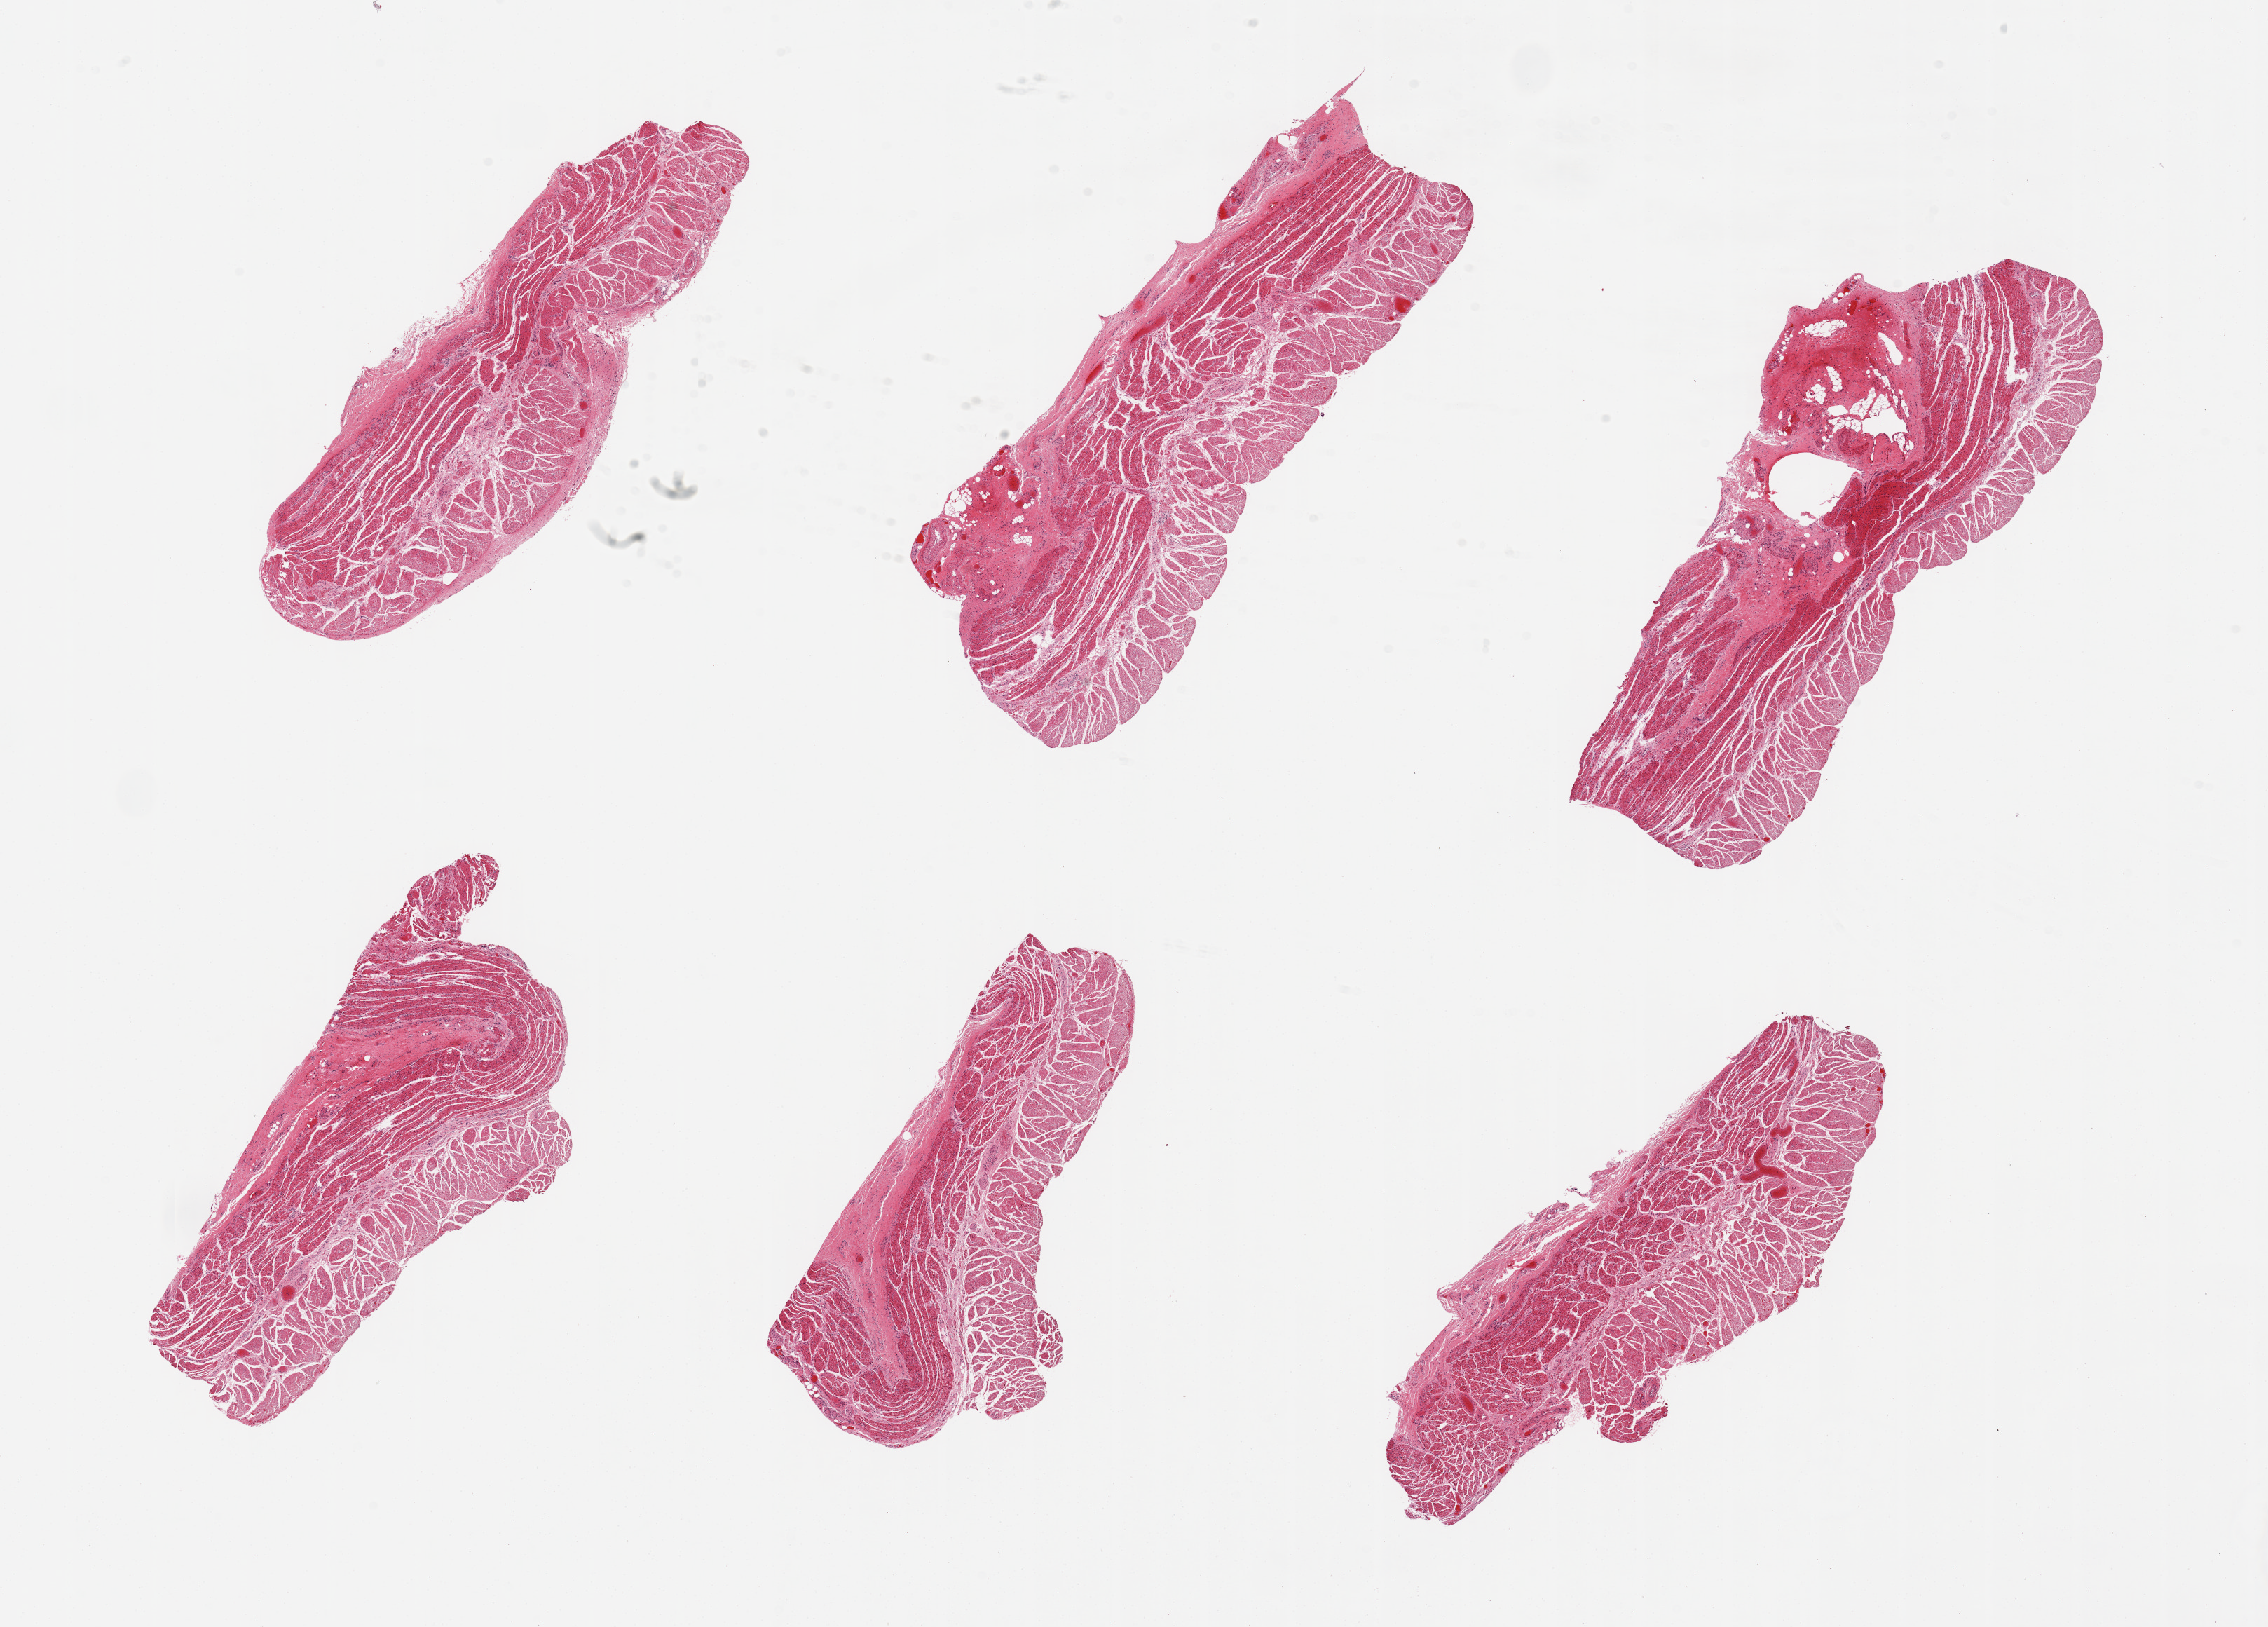
Digitized hematoxylin and eosin (H&E)-stained section, shown as a low-resolution overview of the whole scanned area (about 25.6 x 18.4 mm, from a 20x scan); PAXgene-fixed, paraffin-embedded tissue; section of esophageal muscle (target tissue); tissue donor sample. Donor: male.
Reviewer comment on this tissue sample: 6 pieces. well dissected.